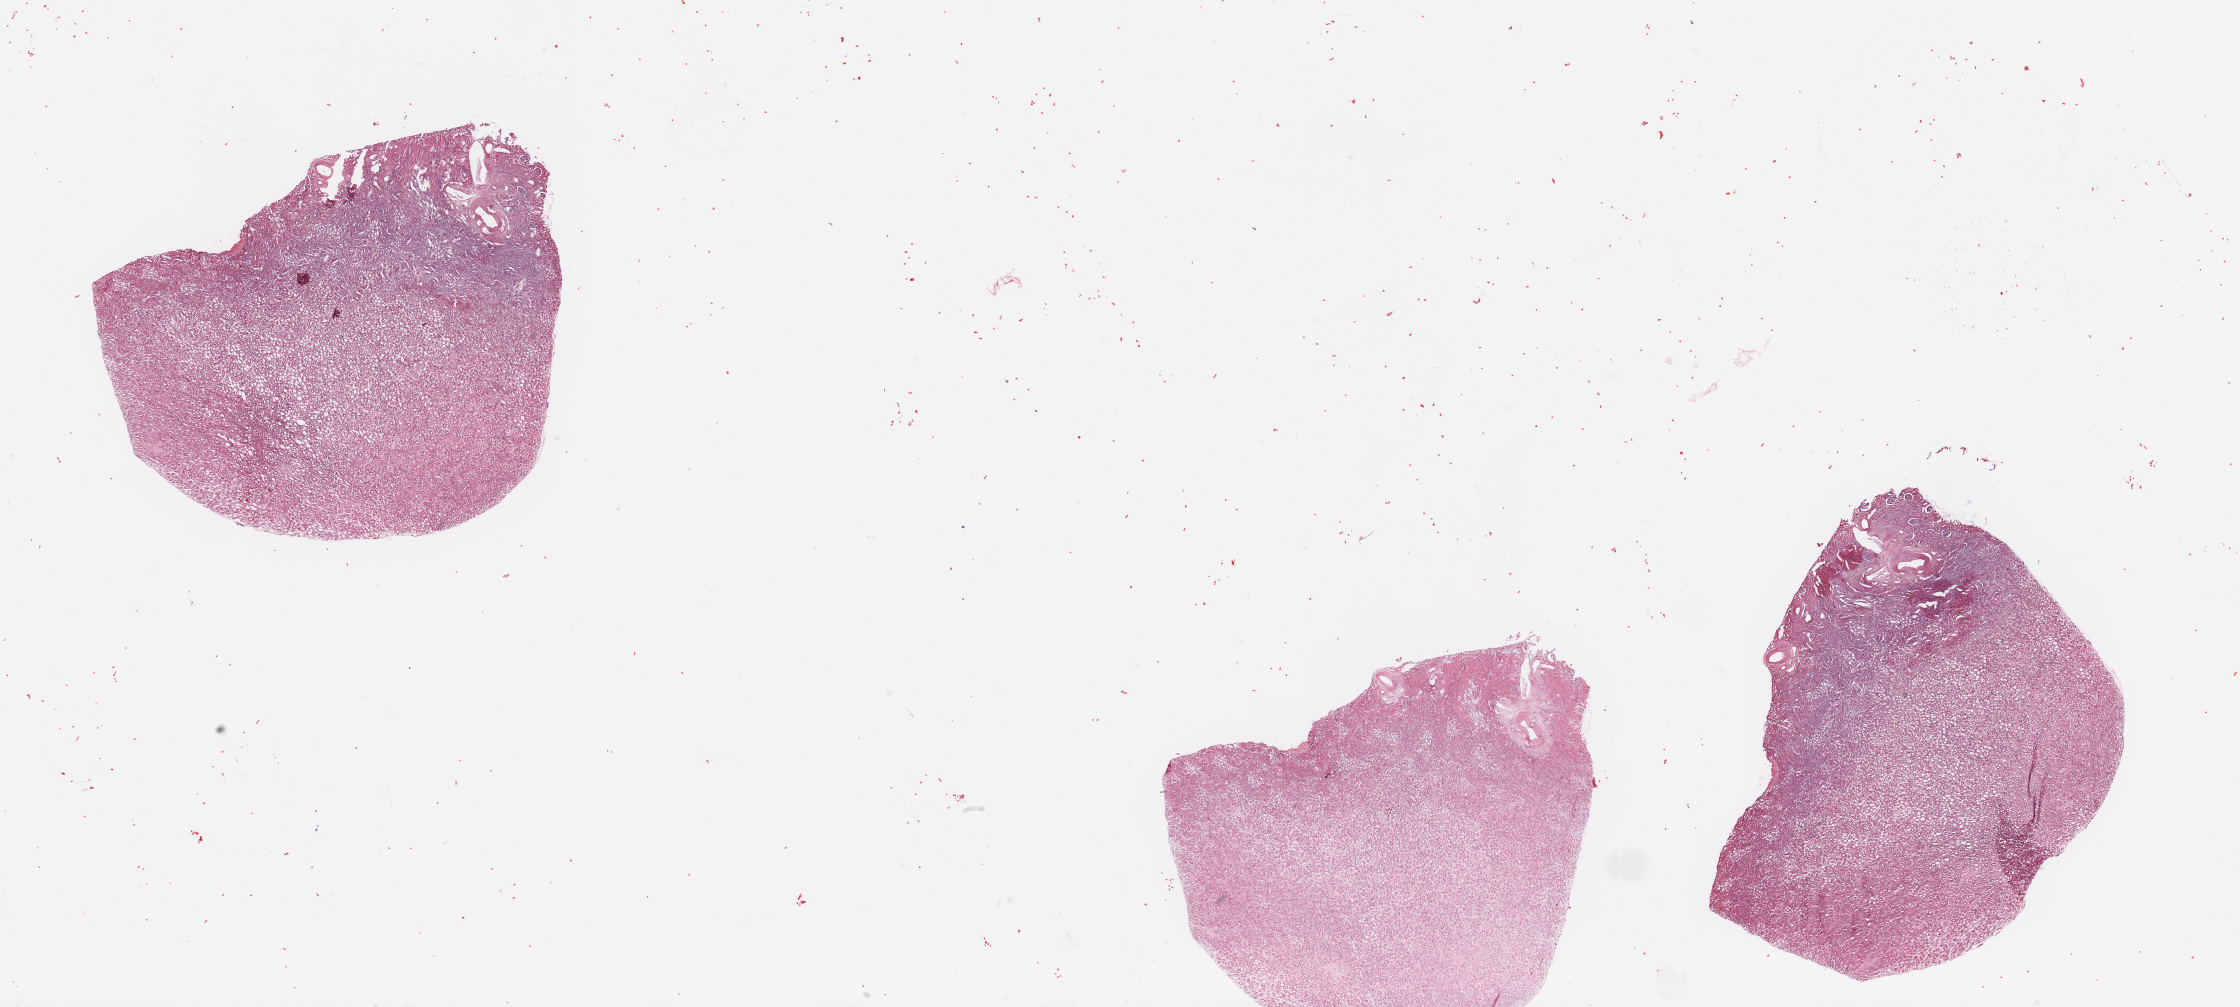
Whole-slide histology image, Hematoxylin and eosin (H&E) stained, whole scanned area (about 35.4 x 15.9 mm, from a 20x scan) shown as a low-resolution overview. Normal (non-tumour) tissue sample, sampled site: kidney. Patient: female, age 55 years.
This section: normal (non-tumour) tissue from the same patient. Patient diagnosis: Renal cell carcinoma, NOS.